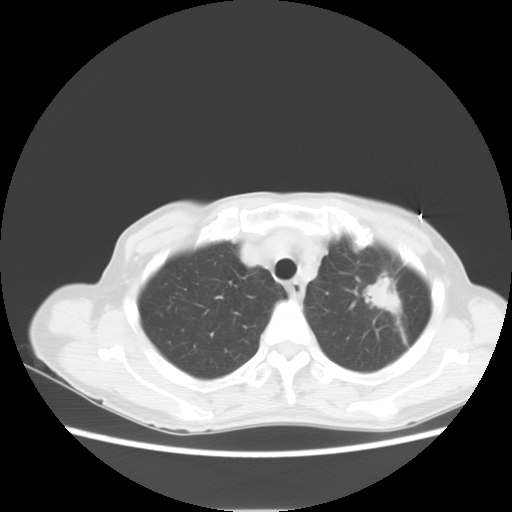
Chest CT, one axial slice; slice 10 of 14 in the series (ordered by position); 120 kVp; lung window (W 1500 / L -600 HU); 5 mm slice thickness; 512 × 512 image matrix, field of view 350 × 350 mm. Patient: female, 71 years. From the clinical record (not read from this slice): clinical TNM (as recorded): T2 N0 M0.
Structures marked on this image (bounding box drawn by a radiologist):
- lung tumour (recorded histology: adenocarcinoma): box from (x=366, y=274) to (x=405, y=317) px